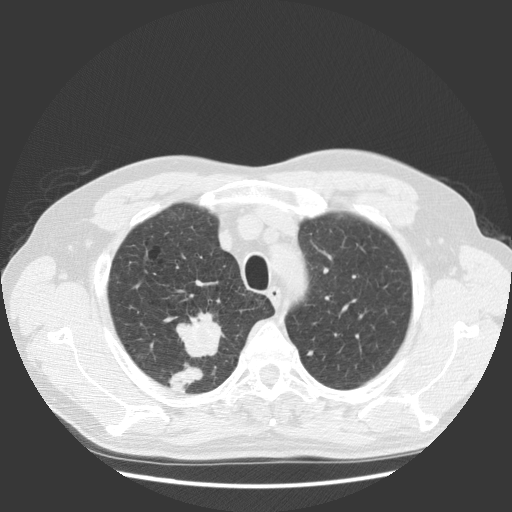
Low-dose screening chest CT, one axial slice; position 103 of 131 along the scan axis; lung window (W 1500 / L -600 HU); 512 × 512 image matrix, field of view 369 × 369 mm.
Outlined on this slice (manually delineated by an expert):
- lesion 1 (tumor, upper lobe of right lung): bounding box (x1, y1, x2, y2) in pixels: (176, 312, 224, 357)
- lesion 2 (tumor, upper lobe of right lung): (169, 363, 203, 390)